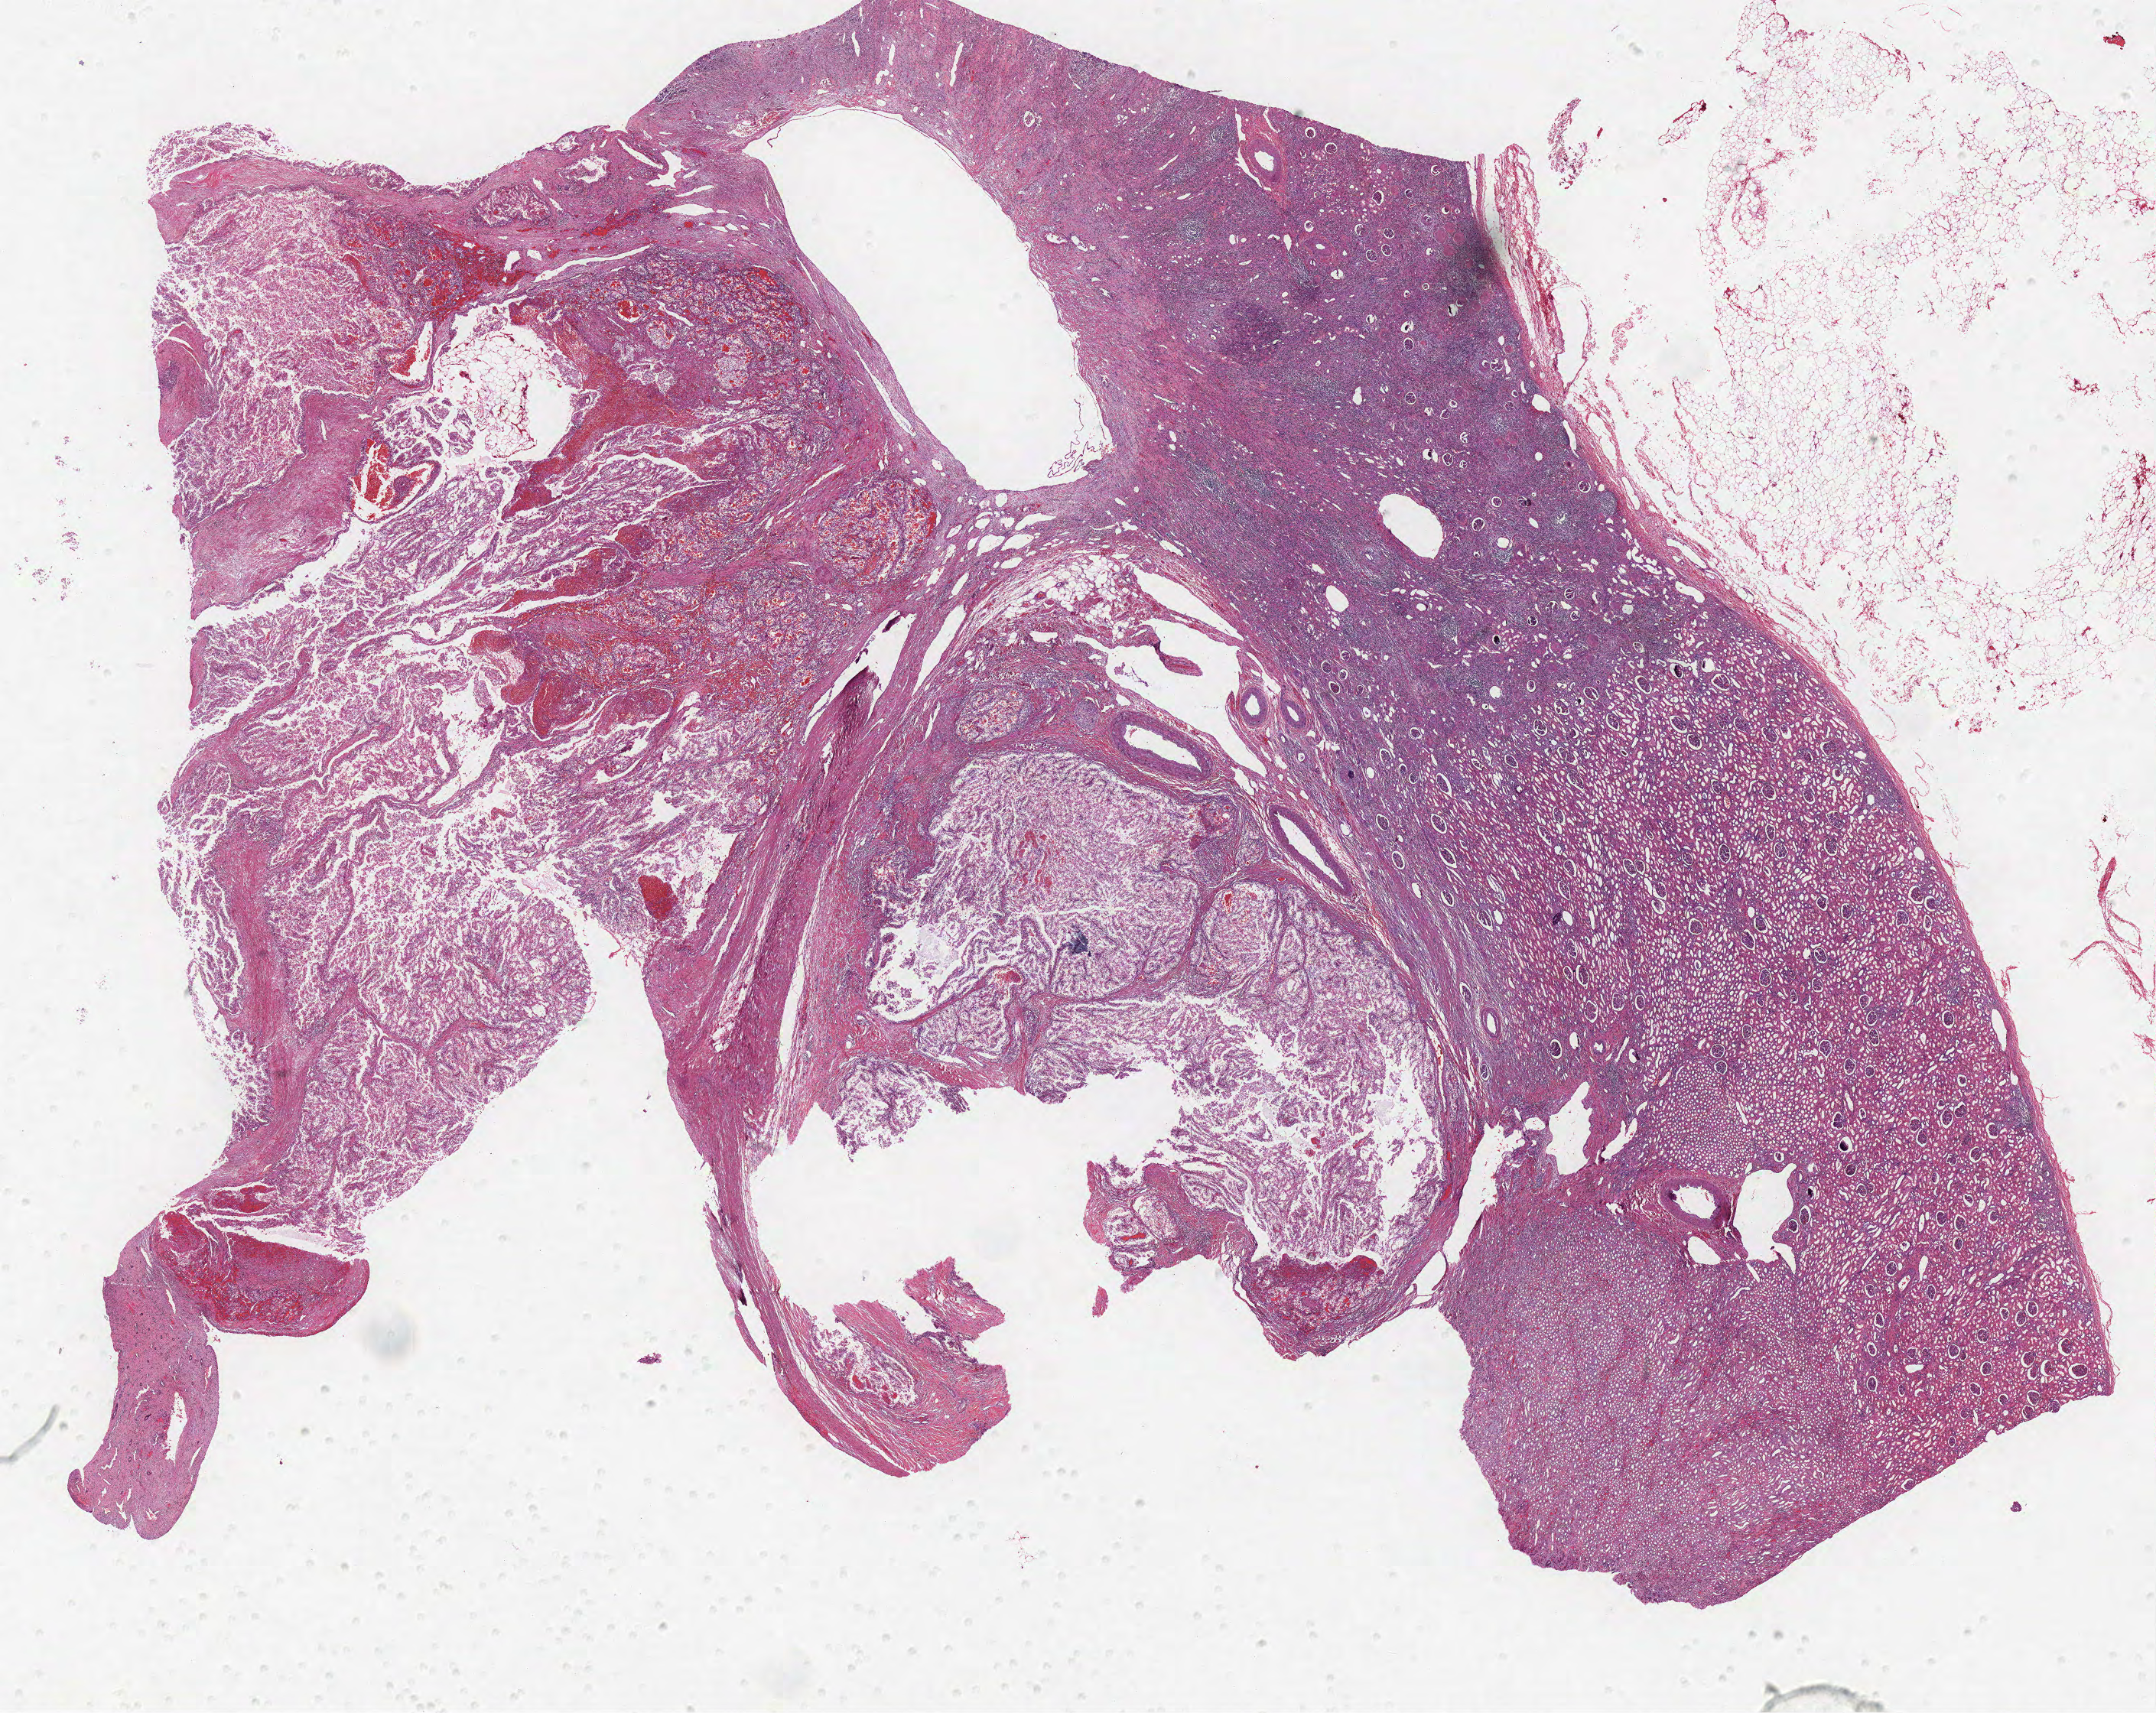
H&E whole-slide image — whole scanned area (about 22.5 x 17.9 mm, acquisition: 40x scan) shown as a low-resolution overview. Formalin-fixed paraffin-embedded (FFPE) diagnostic section. Sample: primary tumour, kidney. Male, age 40 years at initial diagnosis.
Pathologic diagnosis: Clear cell adenocarcinoma, NOS.